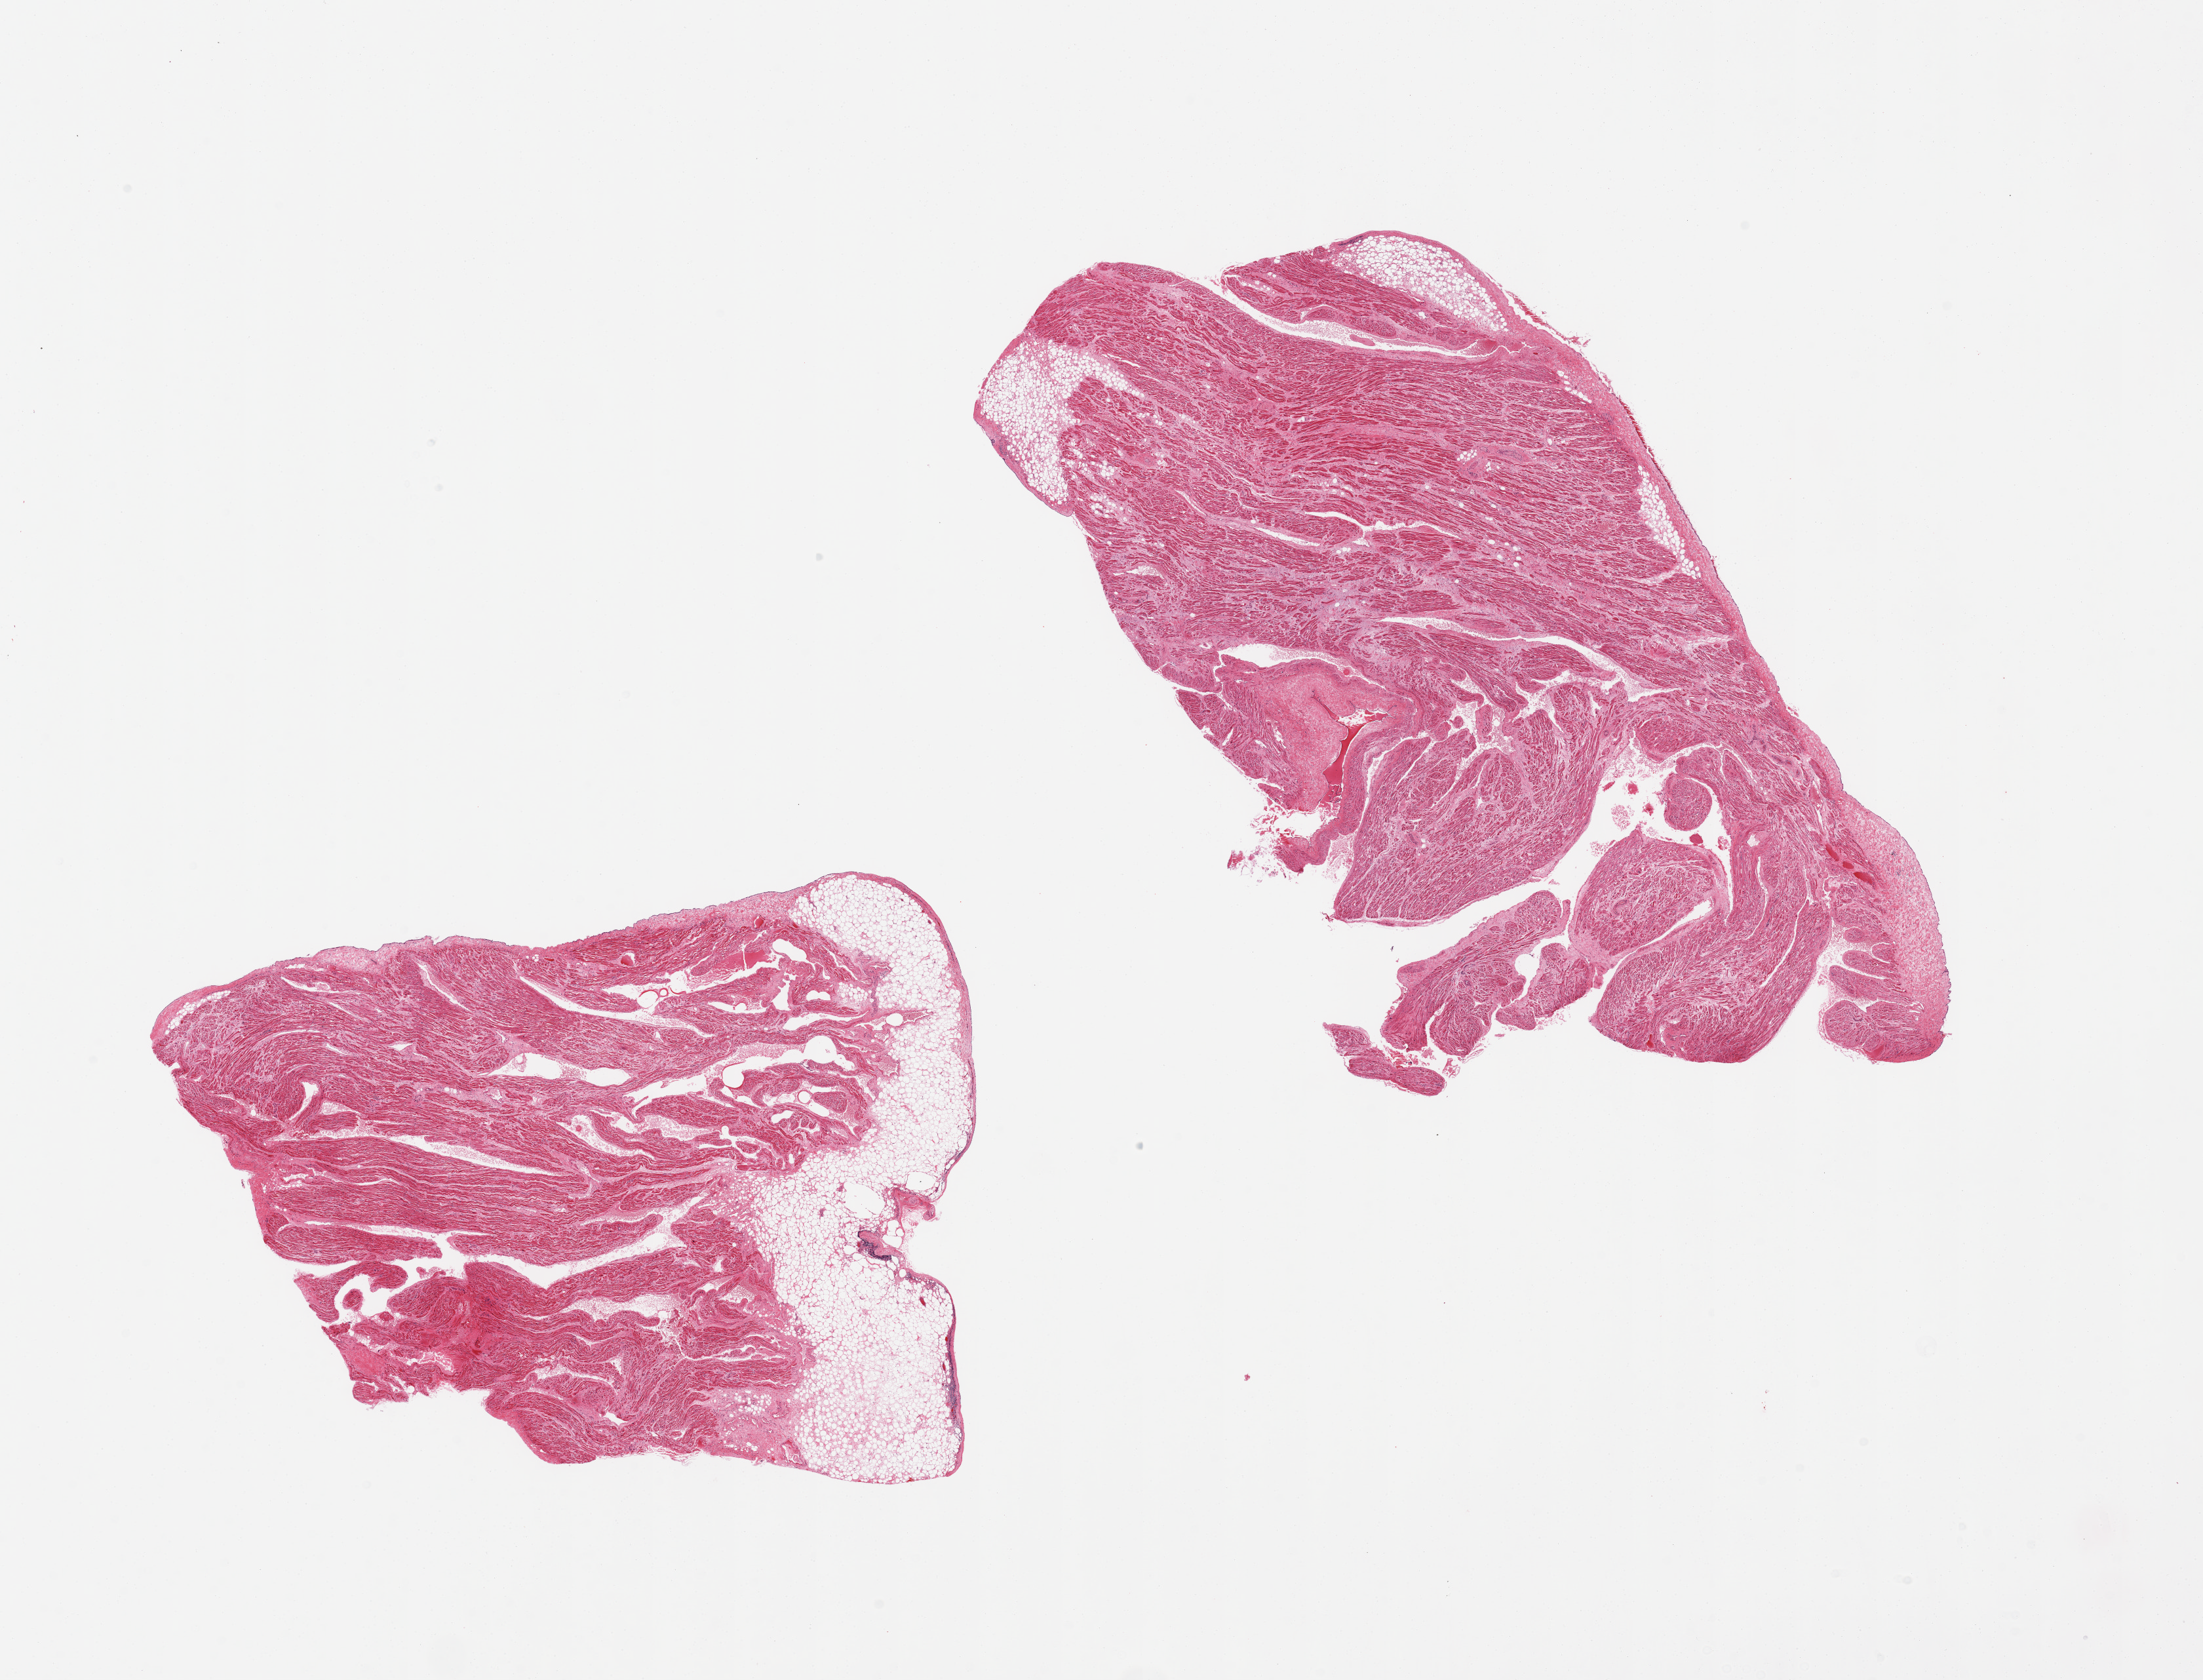
Hematoxylin and eosin (H&E) whole-slide image, low-resolution overview of the scanned area, about 26.6 x 20.3 mm, PAXgene-fixed paraffin-embedded (PFPE) section, sampled site (target tissue): auricular appendage, donor tissue sample. Donor sex: male.
Pathologist's review note for this sample: 2 pieces, one piece is ~20% fat, 2nd ~5% fat.